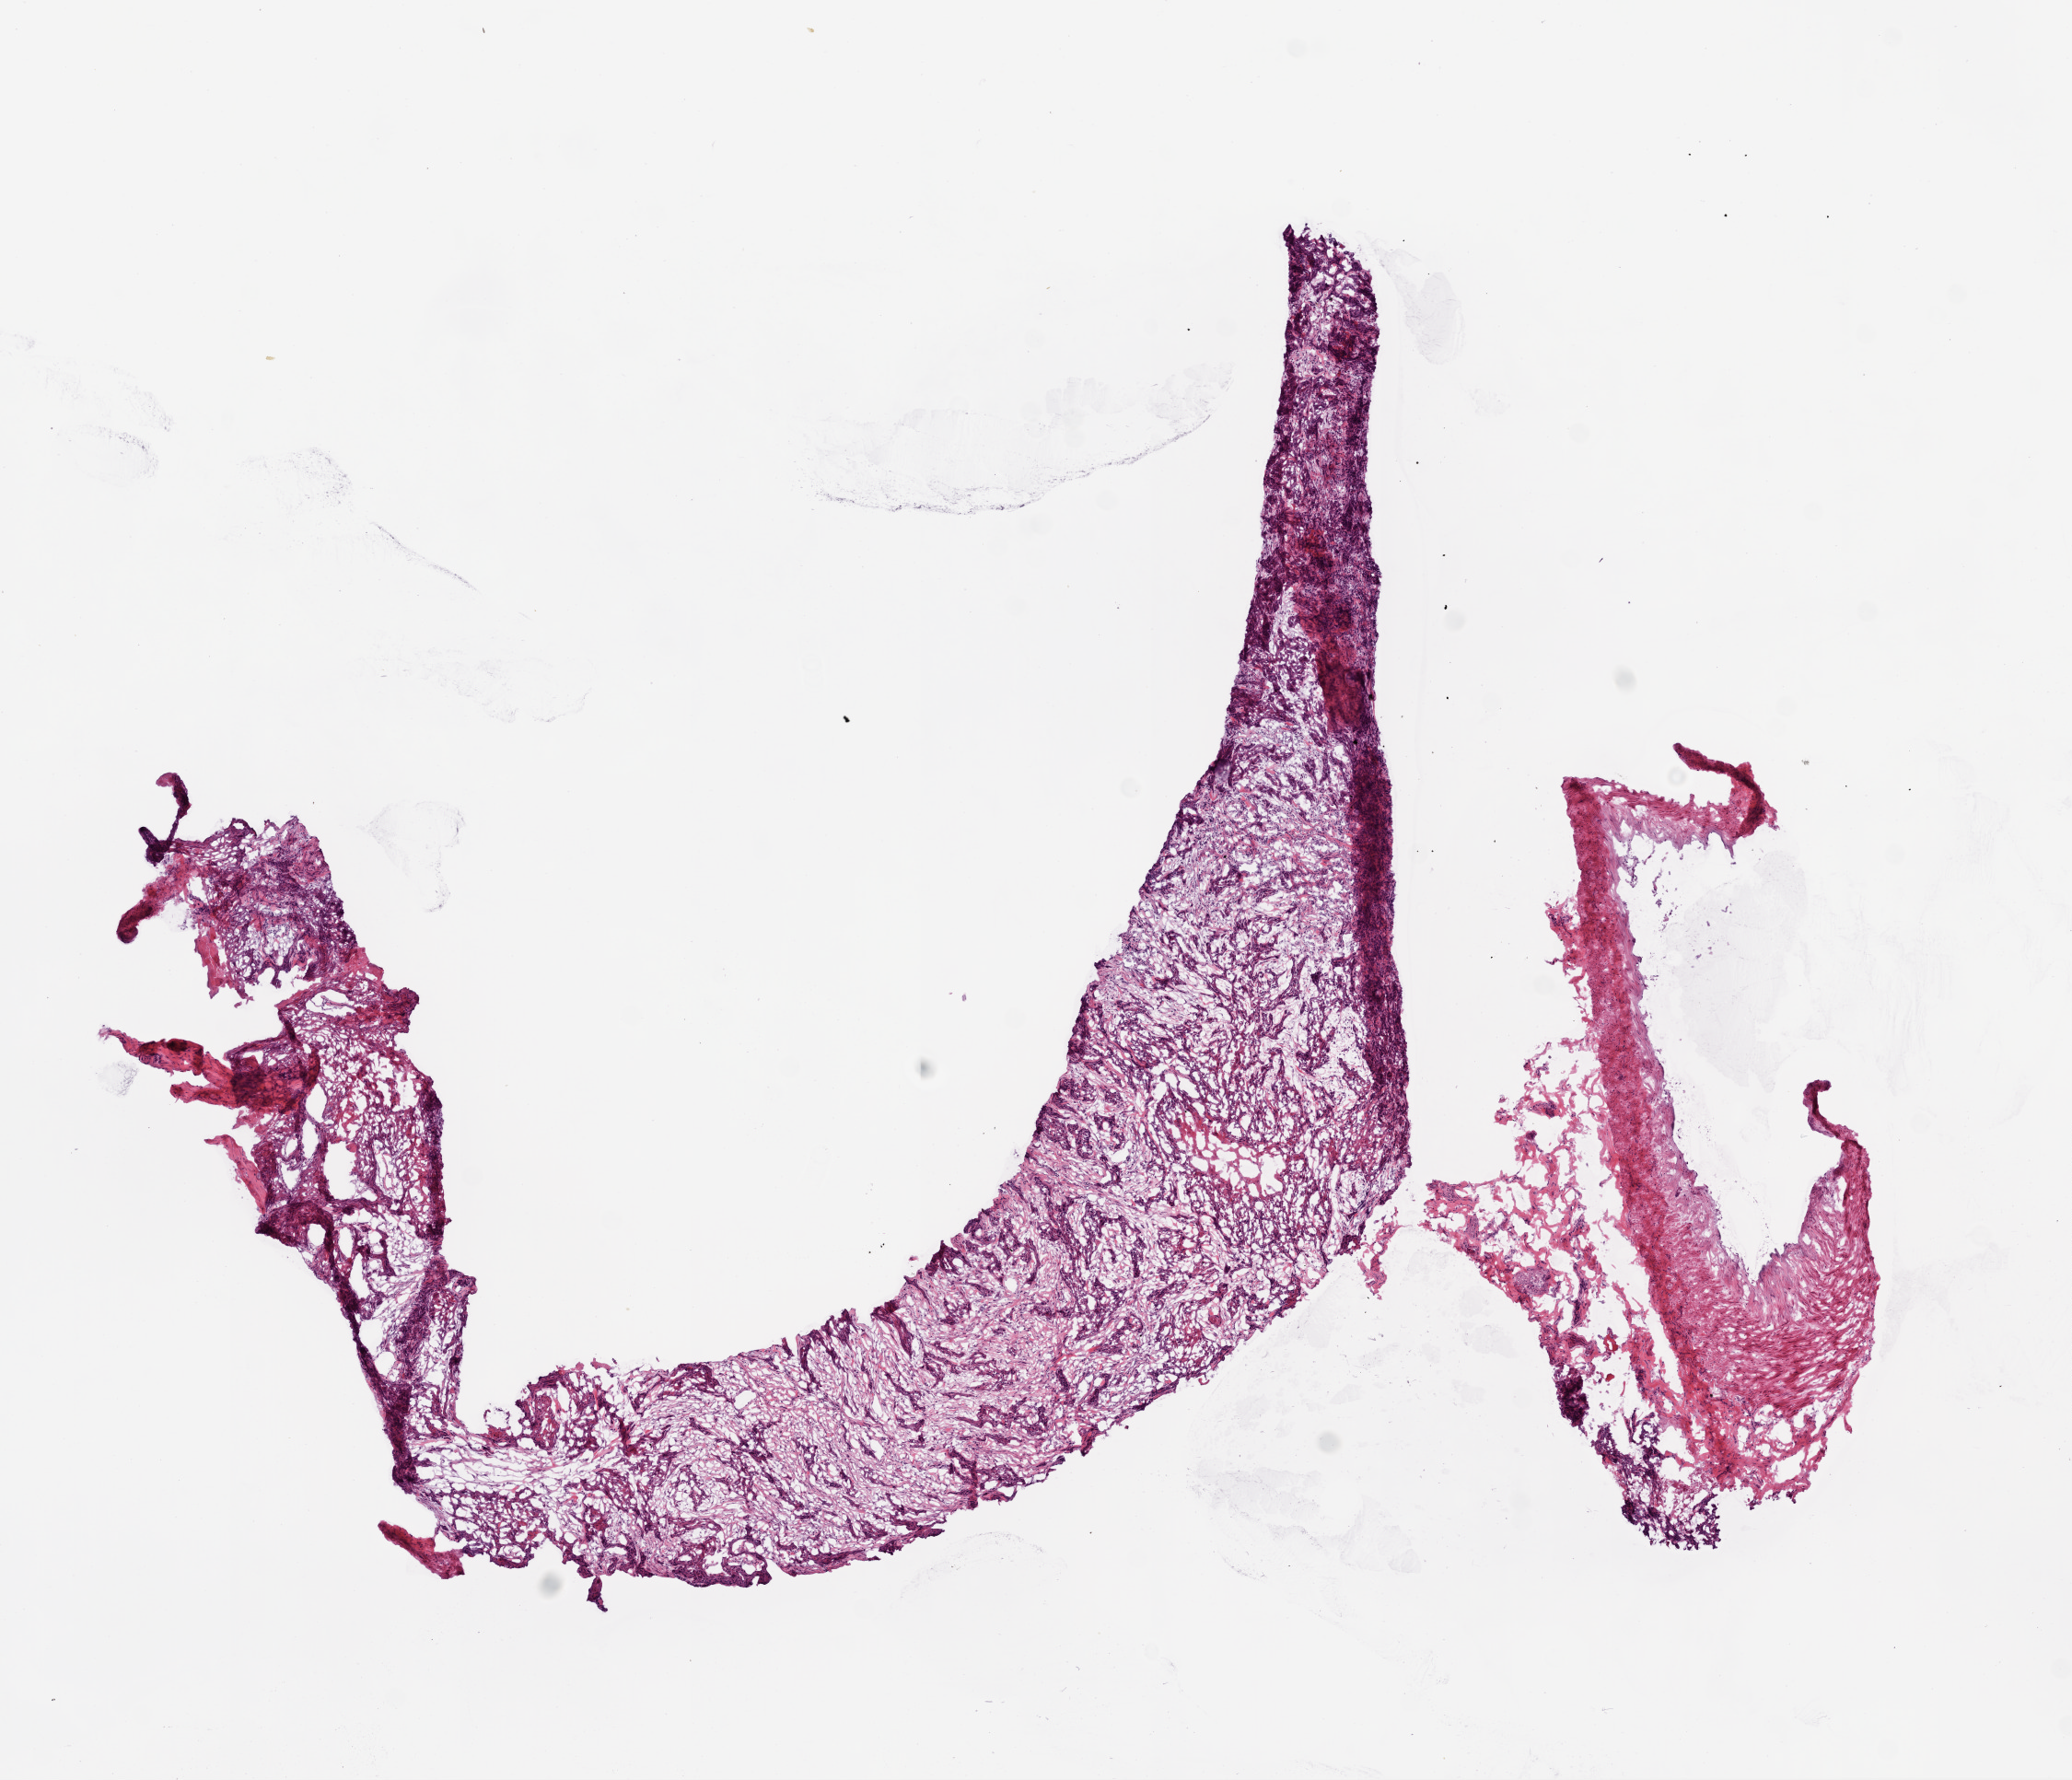
Hematoxylin and eosin (H&E) stained whole-slide image, whole scanned area (about 9.0 x 7.8 mm) shown as a low-resolution overview, frozen section from the top of the tissue portion, primary tumour sample from the head and neck. Female patient; age at initial diagnosis 60 years. Histologic grade: G2 (moderately differentiated). Pathologist review of this section (percent, as recorded): tumour cells 75%, tumour nuclei 75%, normal cells 0%, stromal cells 25%, necrosis 0%.
Pathologic diagnosis: Squamous cell carcinoma, NOS (tongue, NOS). TNM: T4a N2b M0. AJCC pathologic stage: IVA (6th edition).